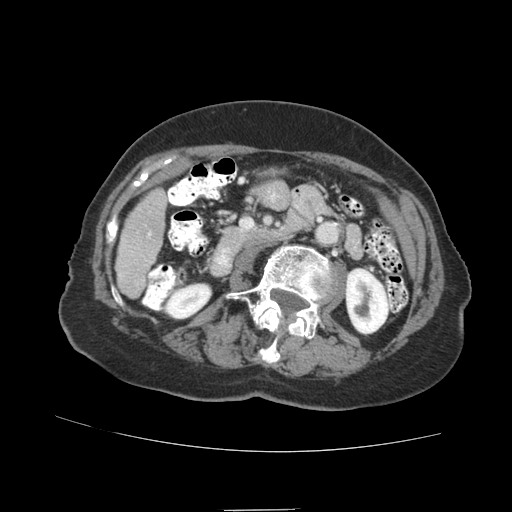
Contrast-enhanced abdominal CT (liver protocol), one axial slice. Slice 21 of 89 in the series (ordered by position). Reconstruction kernel STANDARD. 140 kVp. Soft-tissue window (W 400 / L 40 HU). 2.5 mm slice thickness. 512 × 512 image matrix. Case-level facts recorded for this patient, not image findings: diagnosis: hepatocellular carcinoma (patient treated with transarterial chemoembolisation; whether this scan precedes or follows treatment is not stated here); TNM stage (as recorded): Stage-II; Child-Pugh class: A; tumour nodularity: multinodular.
Annotated regions visible in this slice (semi-automatically segmented with operator editing):
- liver parenchyma outside the tumour (the mass and vessels are separate outlines, so this box may not span the whole liver): bounding box <116,188,166,298> (left, top, right, bottom; pixels)
- liver vessels: <148,233,151,236>